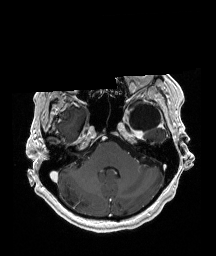
Brain MRI from a brain-tumour surgery series, one axial slice. Position 143 of 192 along the scan axis. T1-weighted post-contrast. 1 mm slice thickness. 216 × 256 image matrix. From the clinical record (not read from this slice): histopathology: Glioblastoma; WHO grade: 4; IDH mutation: no.
Structures marked on this image (outlined manually by an expert reader):
- previous resection cavity: bounding box (x1, y1, x2, y2) in pixels: (130, 104, 161, 131)